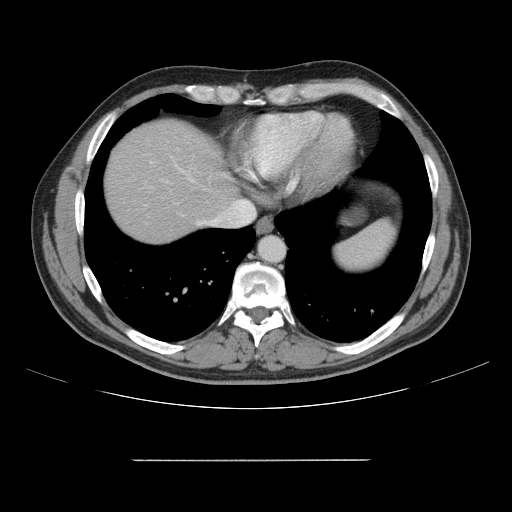
Contrast-enhanced abdominal CT, one axial slice. Position 139 of 164 along the scan axis. Intravenous contrast given. Soft-tissue window (W 400 / L 40 HU). 2.5 mm slice thickness. 512 × 512 image matrix, field of view 404 × 404 mm. Male patient, age 54 years. From the clinical record (not read from this slice): diagnosis: colorectal cancer liver metastases, imaged before liver resection.
Structures marked on this image (manually delineated by an expert):
- hepatic veins: bounding box [x1, y1, x2, y2] px = [188, 177, 255, 226]
- liver: [104, 120, 237, 243]
- planned liver remnant (the part of the liver to remain after resection): [104, 120, 236, 244]
- portal vein (with intrahepatic branches): [181, 170, 189, 175]